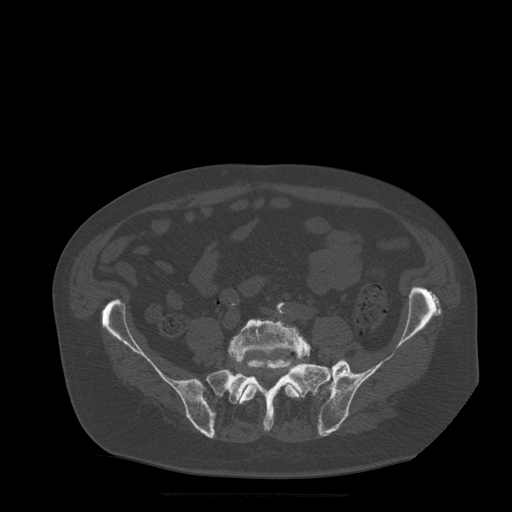
CT including the spine, one axial slice. Position 77 of 522 along the scan axis. Bone window (W 1800 / L 400 HU). 512 × 512 image matrix, field of view 420 × 420 mm. Patient age 72 years. From the clinical record (not read from this slice): primary cancer: prostate.
Annotated regions visible in this slice (semi-automatic segmentation, software-assisted and operator-edited):
- L5 vertebra: bounding box [x1, y1, x2, y2] px = [229, 320, 311, 404]